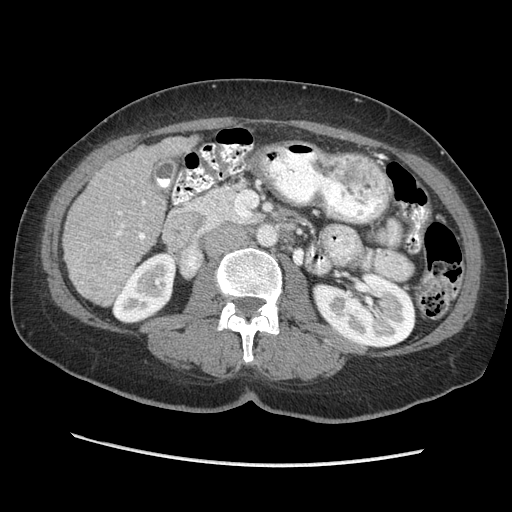
Contrast-enhanced abdominal CT (liver protocol), one axial slice; position 105 of 170 along the scan axis; reconstruction kernel STANDARD; 140 kVp; soft-tissue window (W 400 / L 40 HU); 2.5 mm slice thickness; 512 × 512 image matrix, field of view 360 × 360 mm. From the clinical record (not read from this slice): diagnosis: hepatocellular carcinoma (patient treated with transarterial chemoembolisation; whether this scan precedes or follows treatment is not stated here); TNM stage (as recorded): Stage-II; Child-Pugh class: A; tumour differentiation: no biopsy; tumour nodularity: multinodular.
Annotated regions visible in this slice (semi-automatic segmentation, software-assisted and operator-edited):
- liver parenchyma outside the tumour (the mass and vessels are separate outlines, so this box may not span the whole liver): bounding box [x1, y1, x2, y2] px = [62, 136, 197, 306]
- liver vessels: [115, 201, 146, 240]